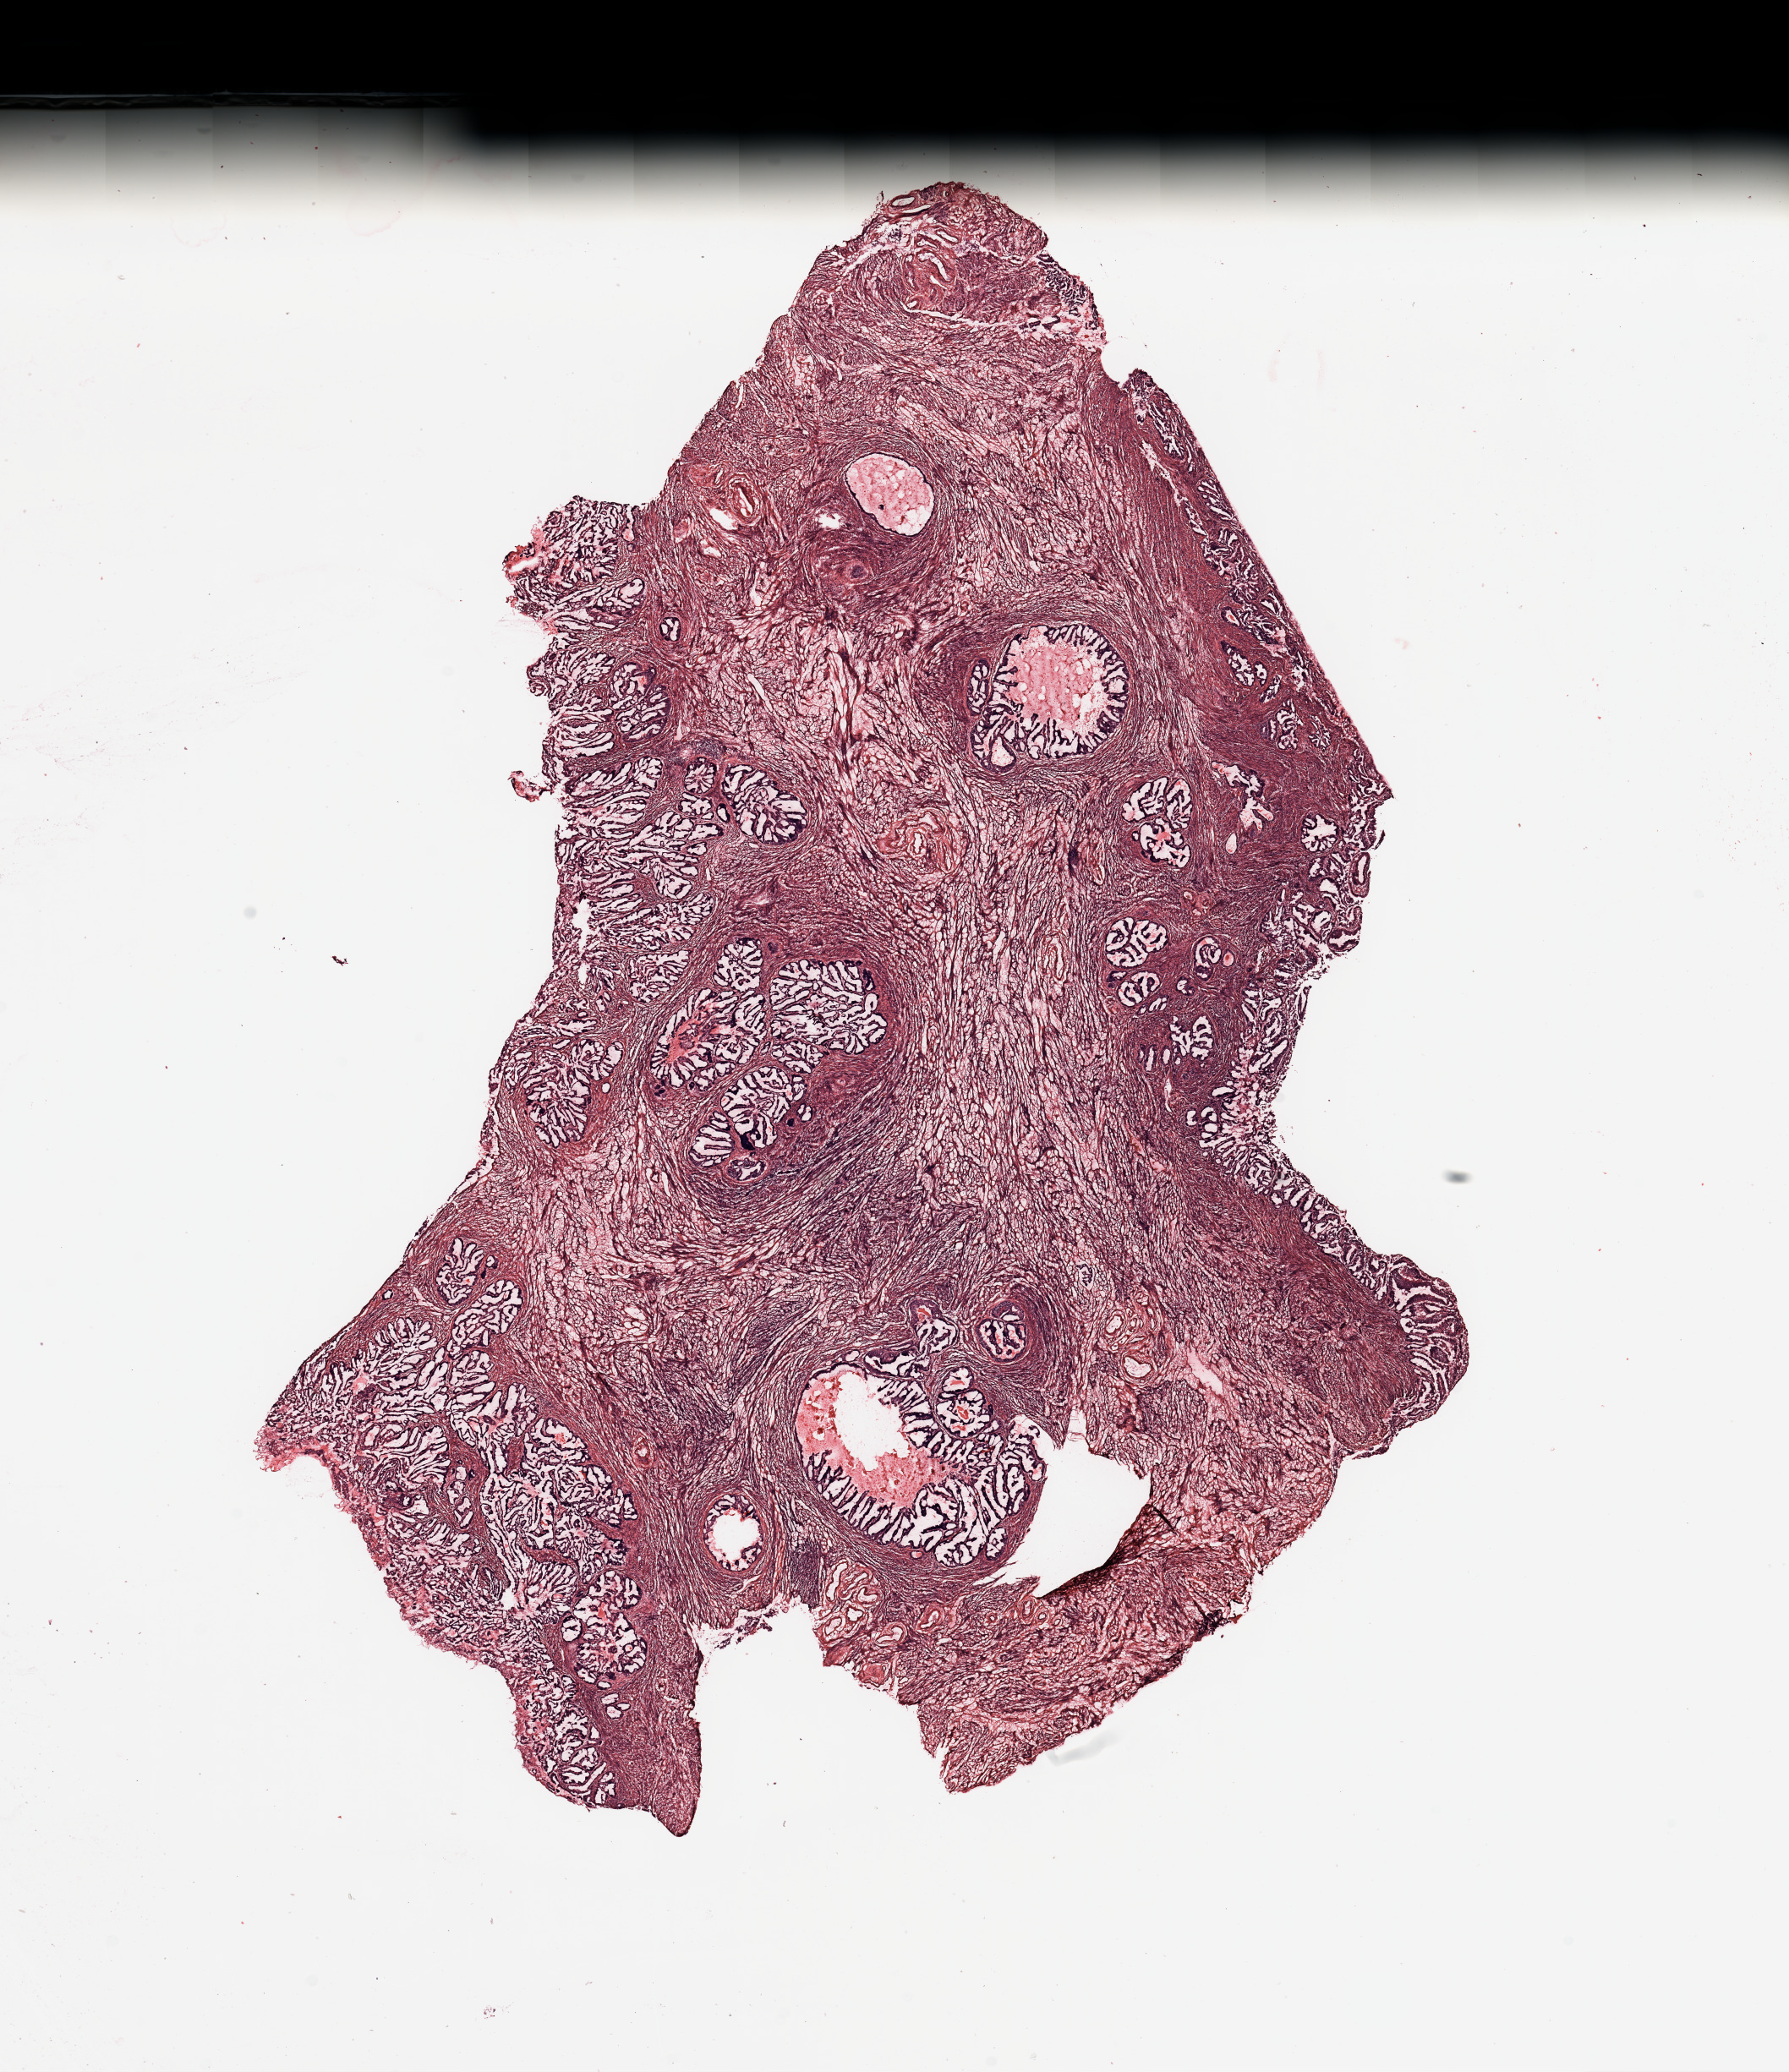
H&E-stained whole-slide image — low-resolution overview of the scanned area, about 16.7 x 19.4 mm (from a 20x scan); uterus, tumour tissue. 70-year-old female patient.
Diagnosis: Endometrioid adenocarcinoma, NOS.